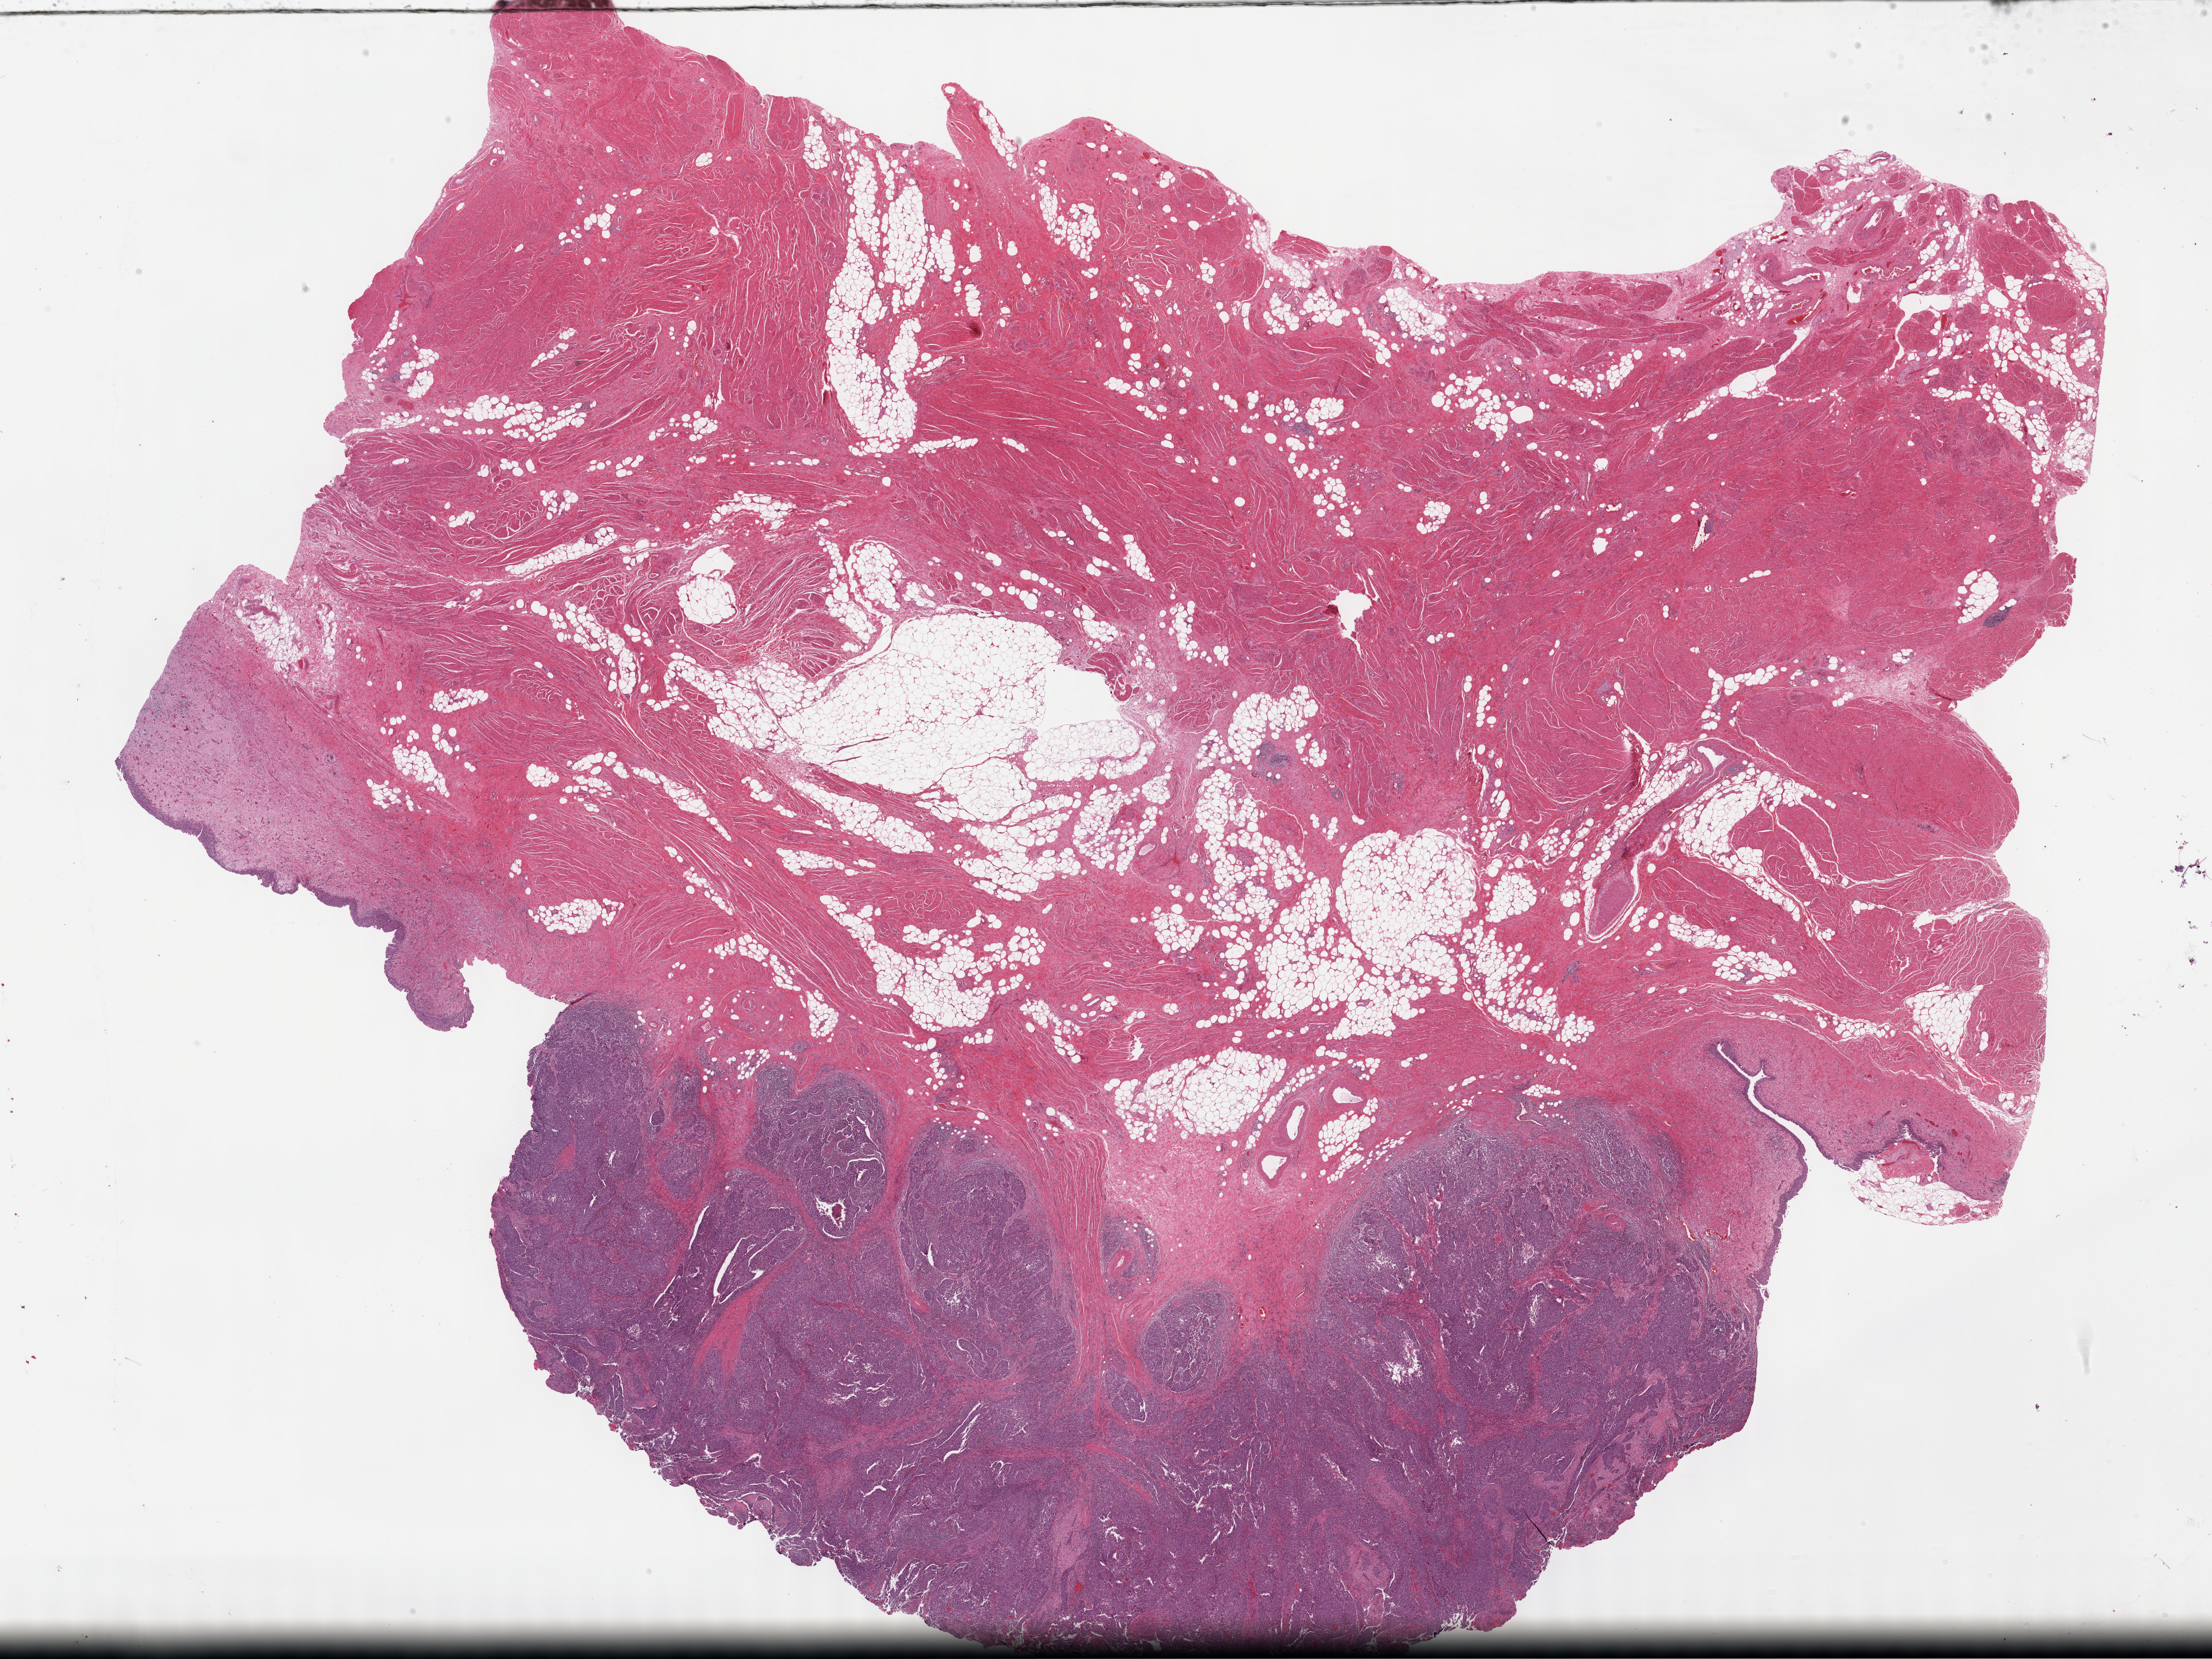
Digitized H&E-stained tissue section (whole slide) — shown as a low-resolution overview of the whole scanned area (about 31.2 x 23.4 mm, slide scanned at 40x), formalin-fixed paraffin-embedded (FFPE) diagnostic section, bladder, primary tumour sample. Male patient; age at initial diagnosis 74 years.
Pathologic diagnosis: Transitional cell carcinoma.